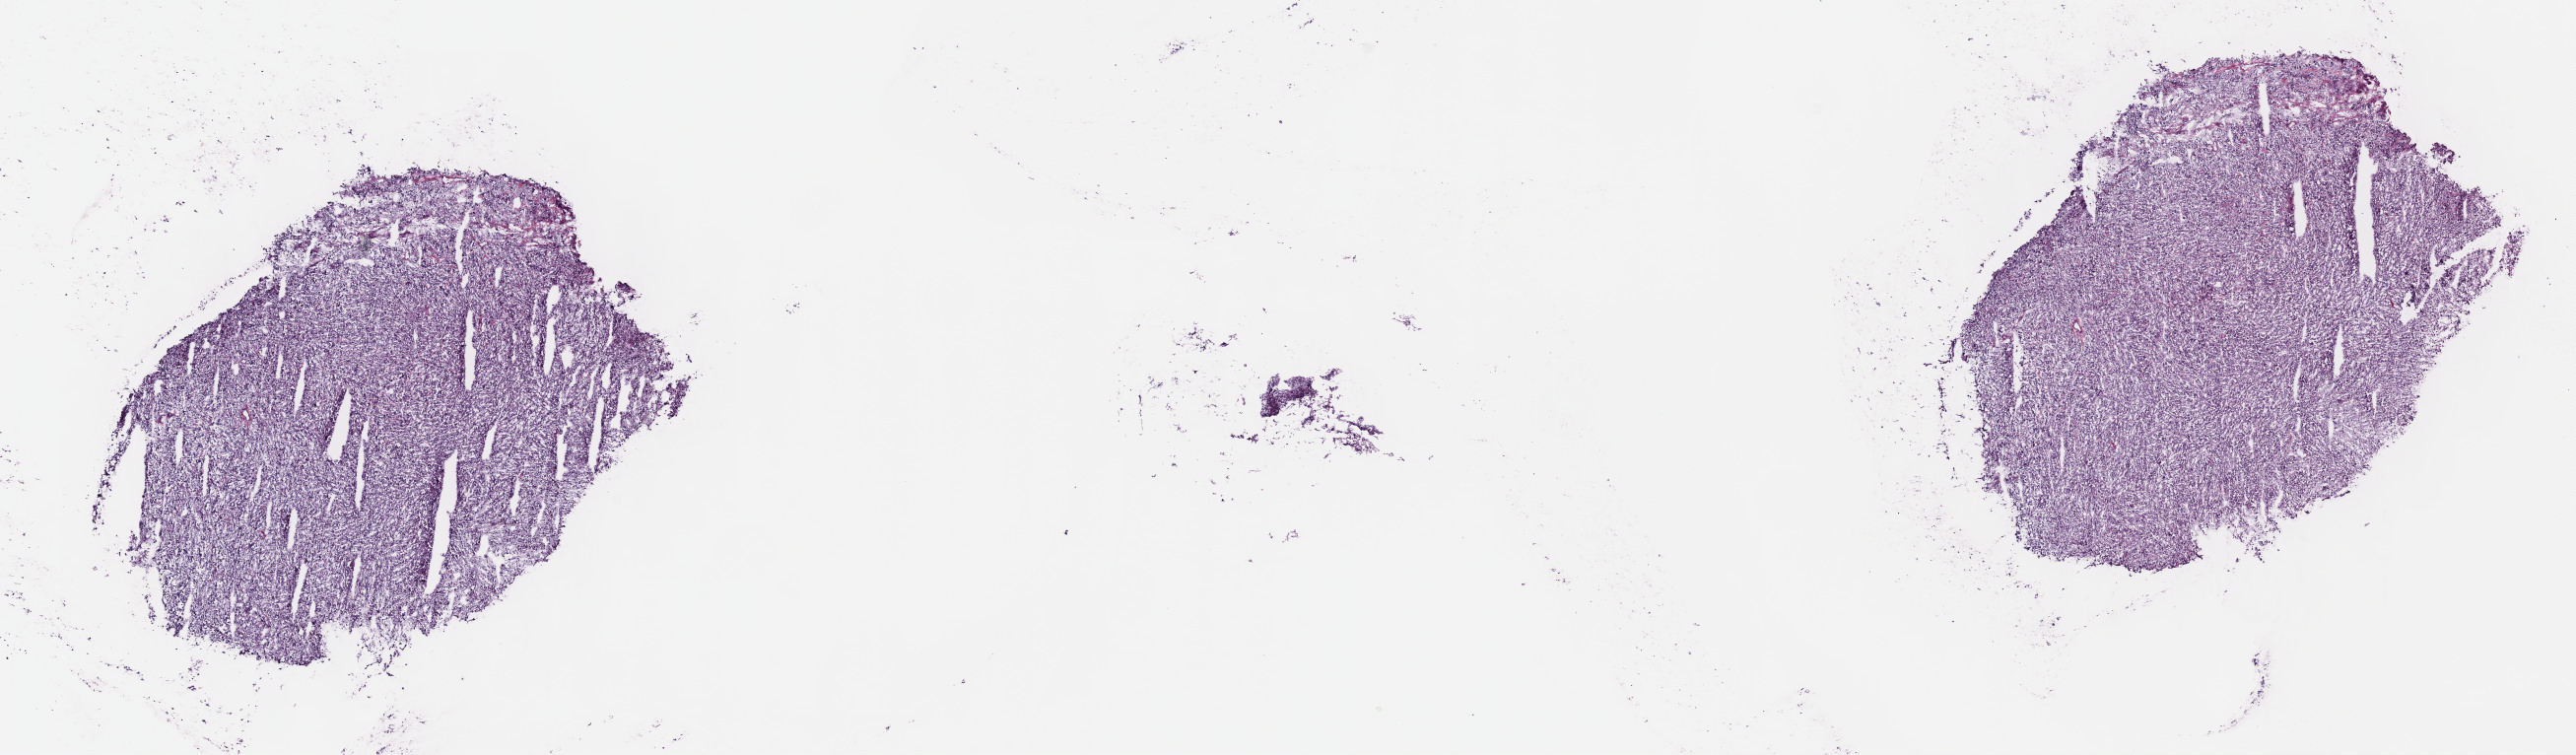
Whole-slide histology image, H&E, low-resolution overview of the scanned area, about 21.1 x 6.2 mm (acquisition: 40x scan). Frozen section from the top of the tissue portion. Primary tumour sample from the adrenal gland. Female, age 76 years at initial diagnosis. Pathologist review of this section (percent, as recorded): tumour cells 85%, tumour nuclei 85%, normal cells 0%, stromal cells 15%, necrosis 0%. Infiltration values recorded for this section: lymphocyte infiltration 1%, monocyte infiltration 1%, neutrophil infiltration 1%.
Pathologic diagnosis: Pheochromocytoma, NOS. Laterality: right.